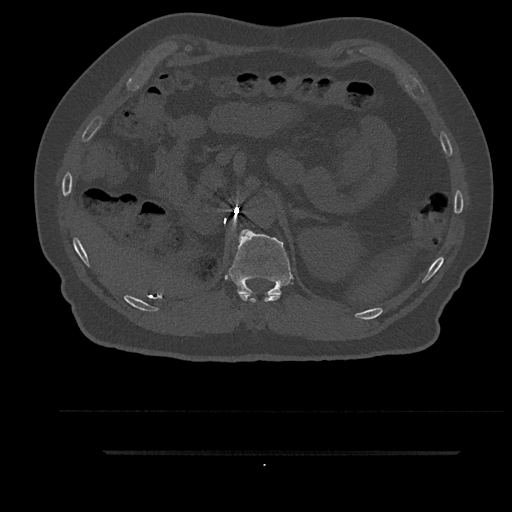
CT including the spine, one axial slice. Slice 264 of 797 in the series (ordered by position). 120 kVp. Bone window (W 1800 / L 400 HU). 0.5 mm slice thickness. 512 × 512 image matrix. Patient: male, 63 years. From the clinical record (not read from this slice): primary cancer: renal; vertebrae with lytic lesions (as recorded): T8.
Outlined on this slice (semi-automatic segmentation, software-assisted and operator-edited):
- T11 vertebra: box from (x=239, y=294) to (x=281, y=303) px
- T12 vertebra: (x=228, y=229)–(x=293, y=298)